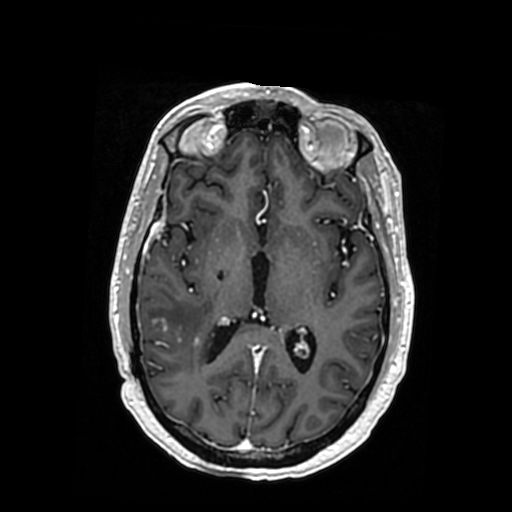
Brain MRI from a brain-tumour surgery series, one axial slice. Slice 183 of 364 in the series (ordered by position). T1-weighted post-contrast. 512 × 512 image matrix, field of view 260 × 260 mm. From the clinical record (not read from this slice): histopathology: Oligodendroglioma; WHO grade: 3.
Outlined on this slice (expert manual segmentation):
- tumour: bounding box (x1, y1, x2, y2) in pixels: (146, 316, 217, 342)